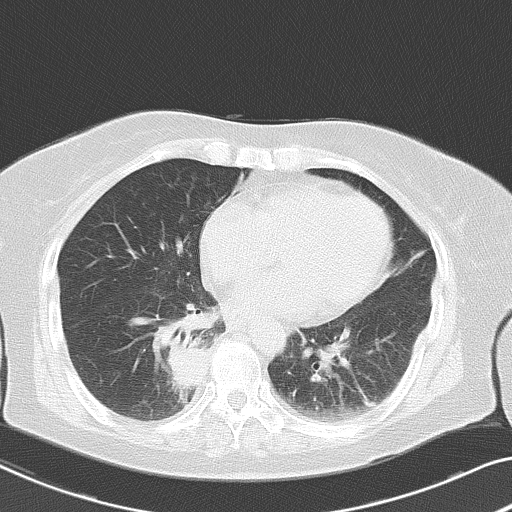
Chest CT, one axial slice; position 20 of 53 along the scan axis; reconstruction kernel B70f; lung window (W 1500 / L -600 HU); 5 mm slice thickness; 512 × 512 image matrix. Patient: female, 70 years. Case-level facts recorded for this patient, not image findings: clinical TNM (as recorded): T2 N1 M1a.
Annotated regions visible in this slice (bounding box drawn by a radiologist):
- lung tumour (recorded histology: adenocarcinoma): bounding box (x1, y1, x2, y2) in pixels: (154, 332, 209, 400)